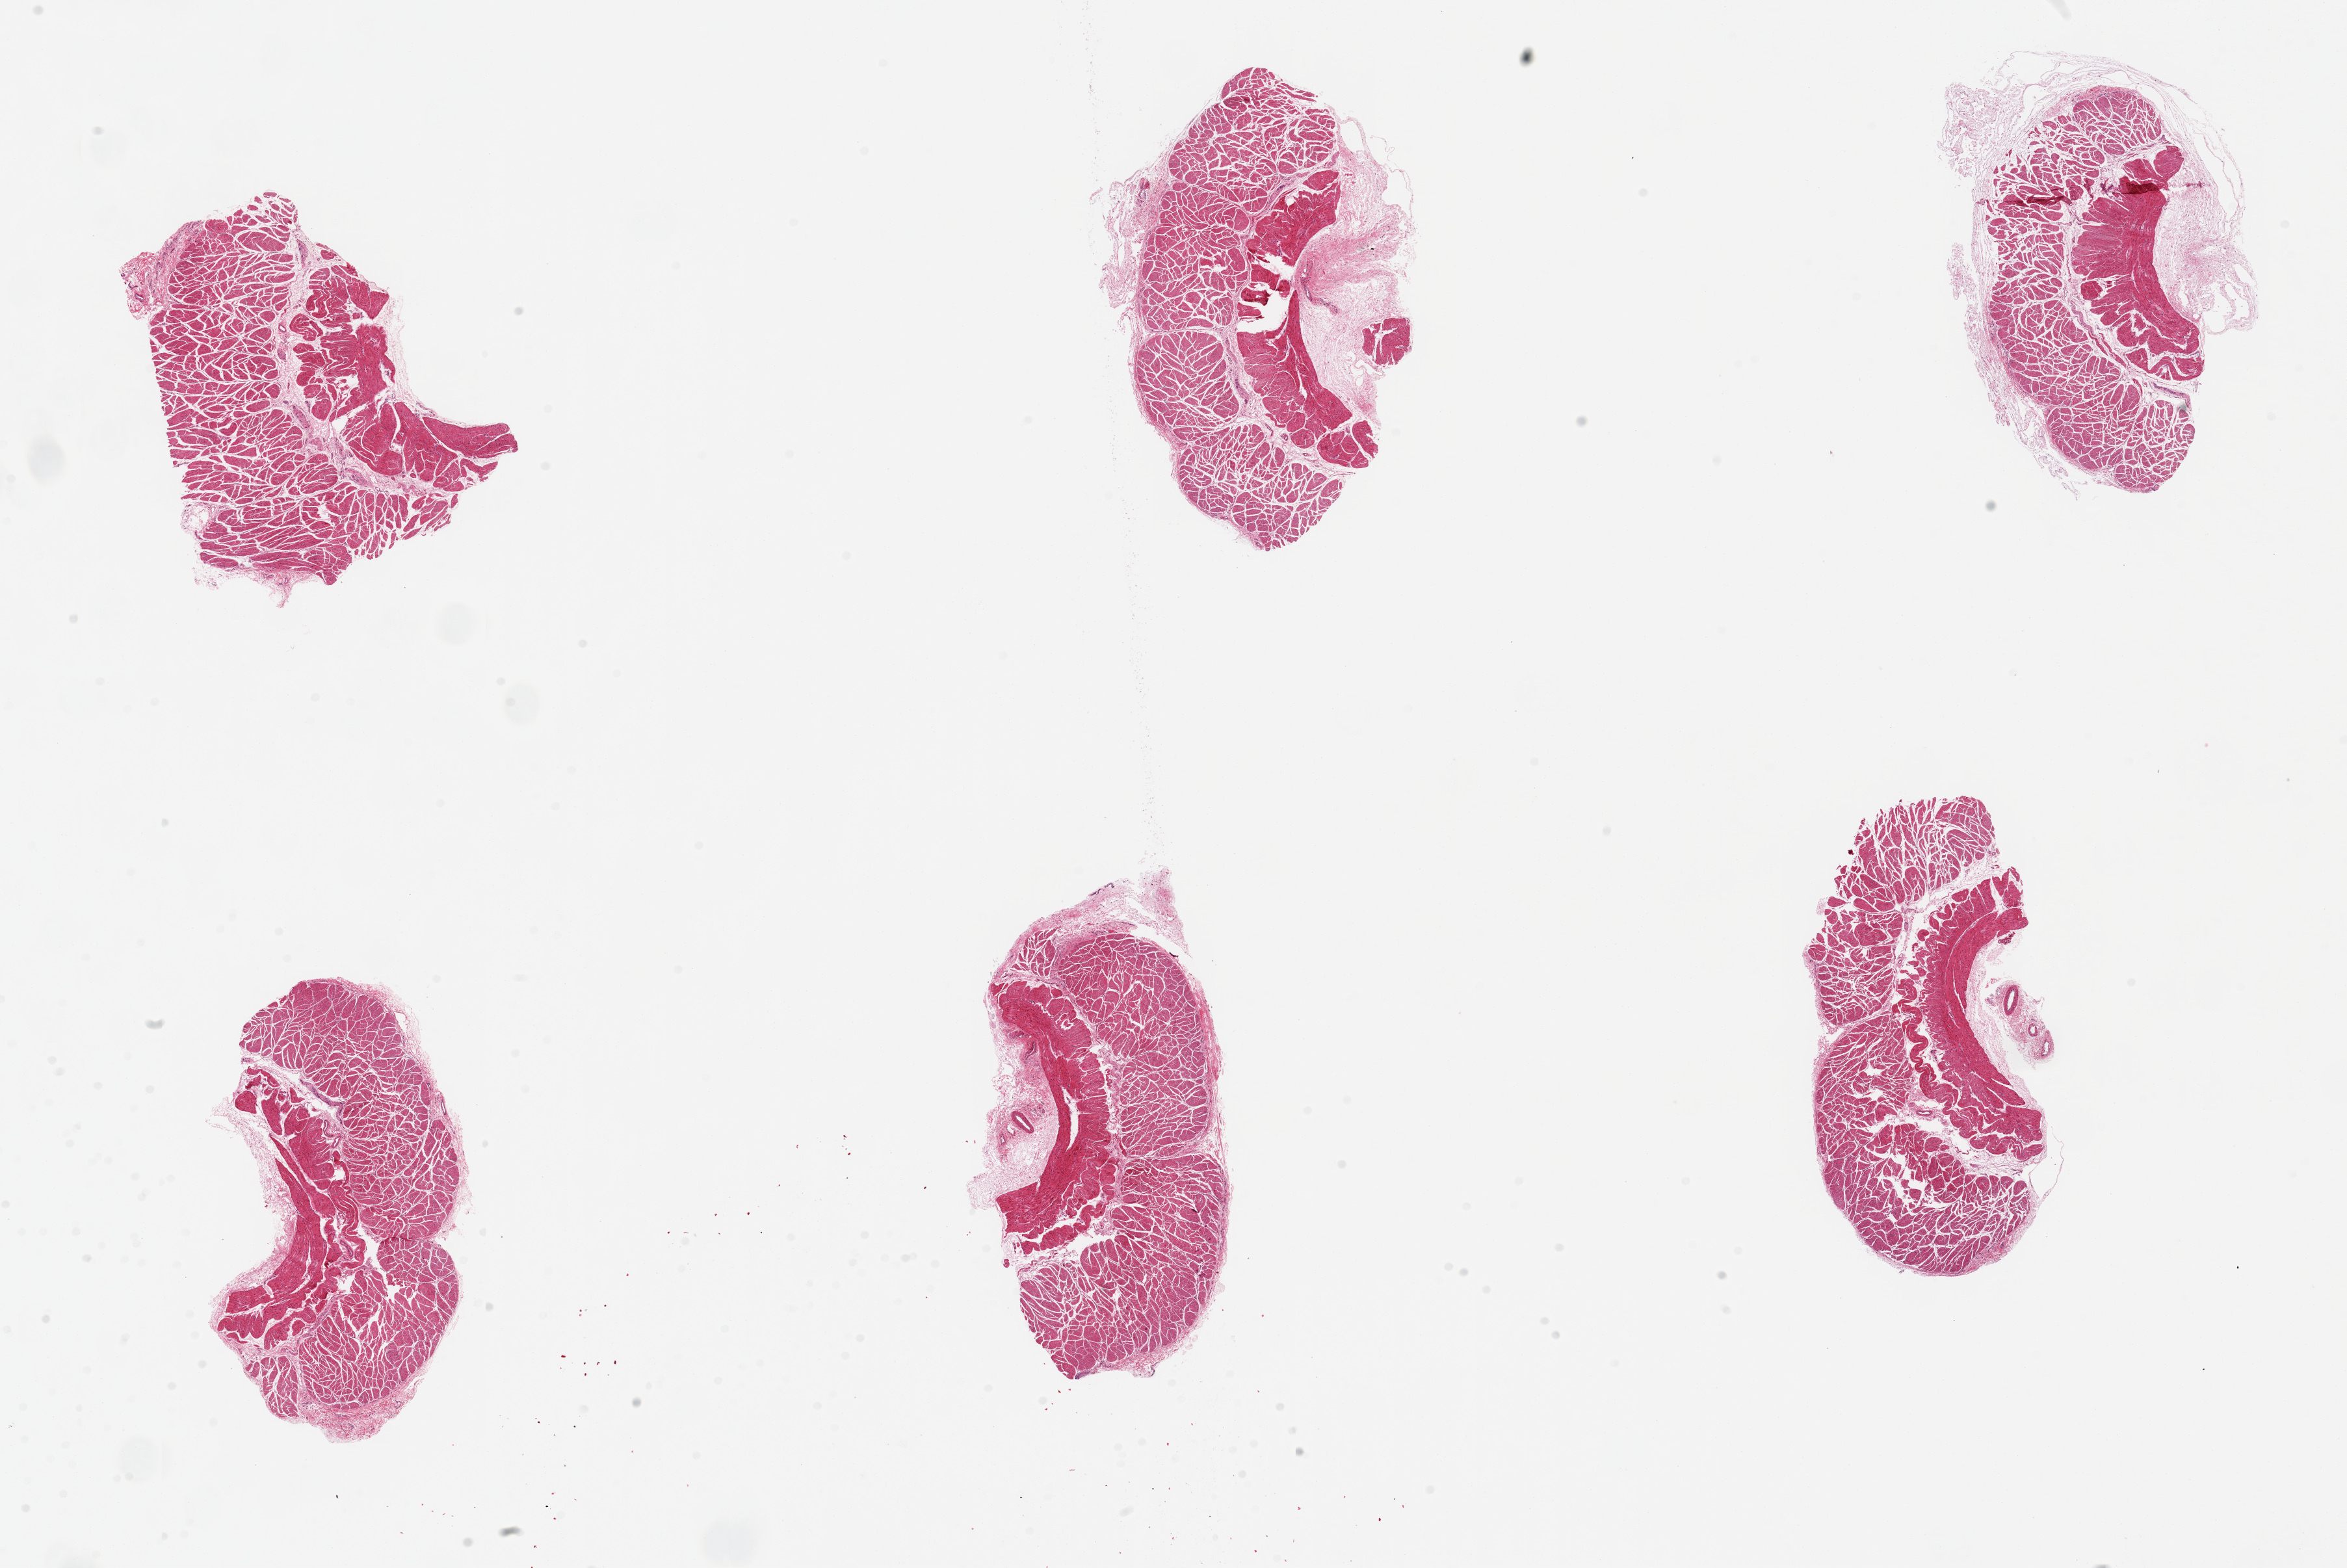
Digitized haematoxylin and eosin-stained section, brightfield — shown as a low-resolution overview of the whole scanned area (about 28.5 x 19.1 mm, slide scanned at 20x), PAXgene-fixed, paraffin-embedded tissue, sampled site (target tissue): esophageal muscle, tissue donor sample.
Pathologist's review note for this sample: 6 pieces, up to 6x3mm; trace adherent serosal connective tissue.